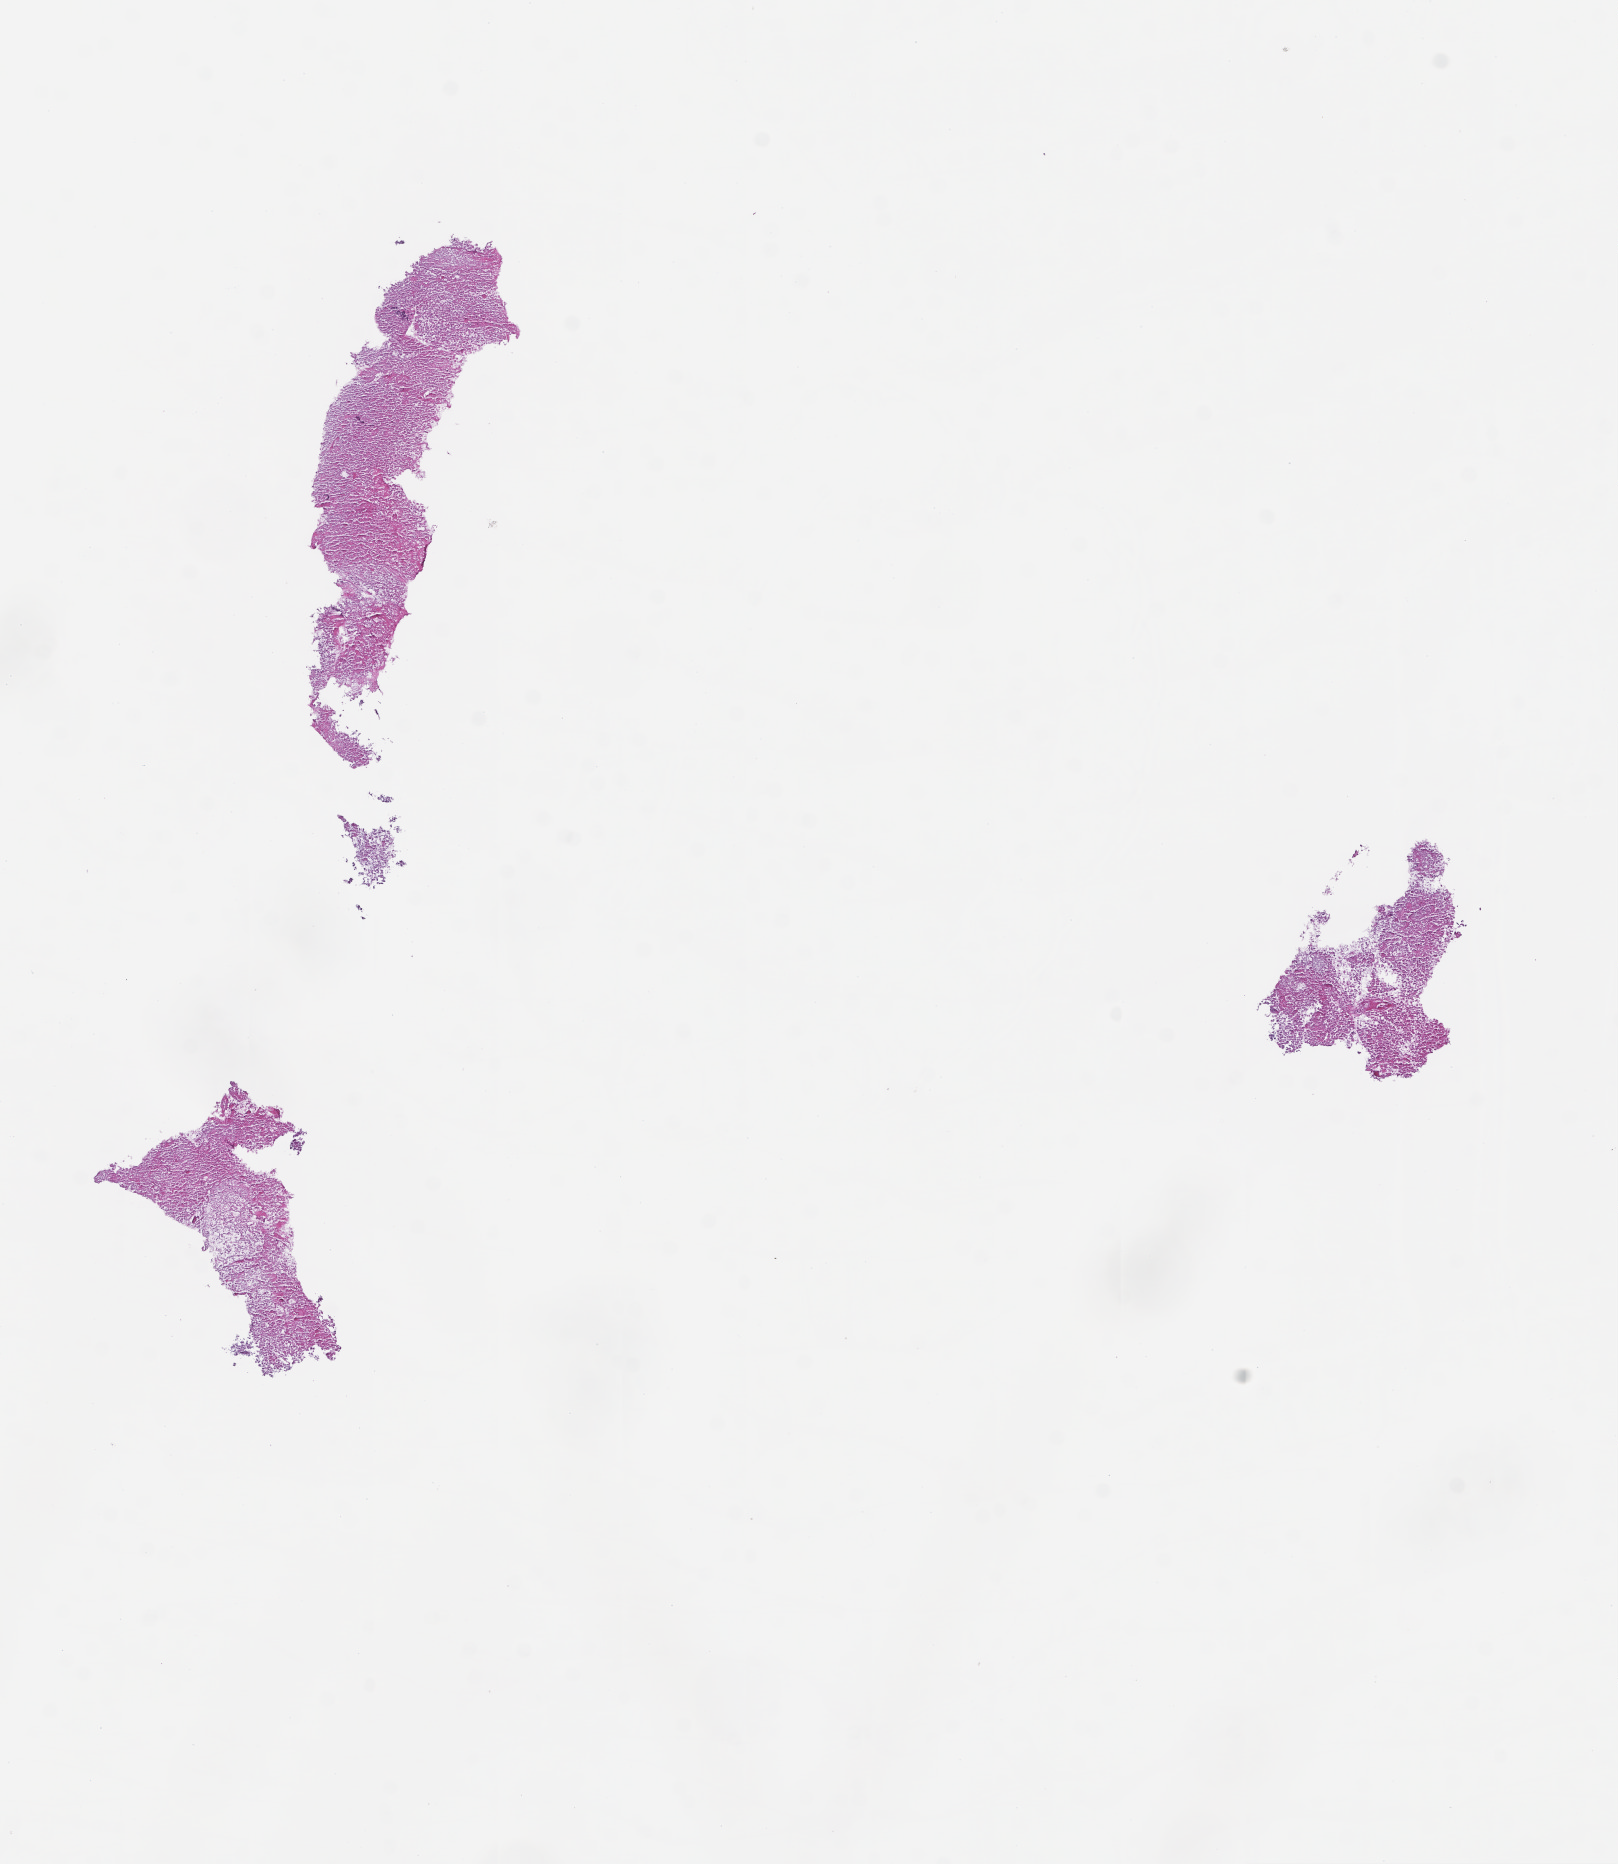
Digitized hematoxylin and eosin (H&E)-stained section, whole scanned area (about 6.5 x 7.5 mm) shown as a low-resolution overview, formalin-fixed paraffin-embedded section, specimen time point: collected at baseline (before treatment). Patient sex: female.
This section: metastatic tumor tissue. Primary diagnosis of the patient: Colorectal Carcinoma.